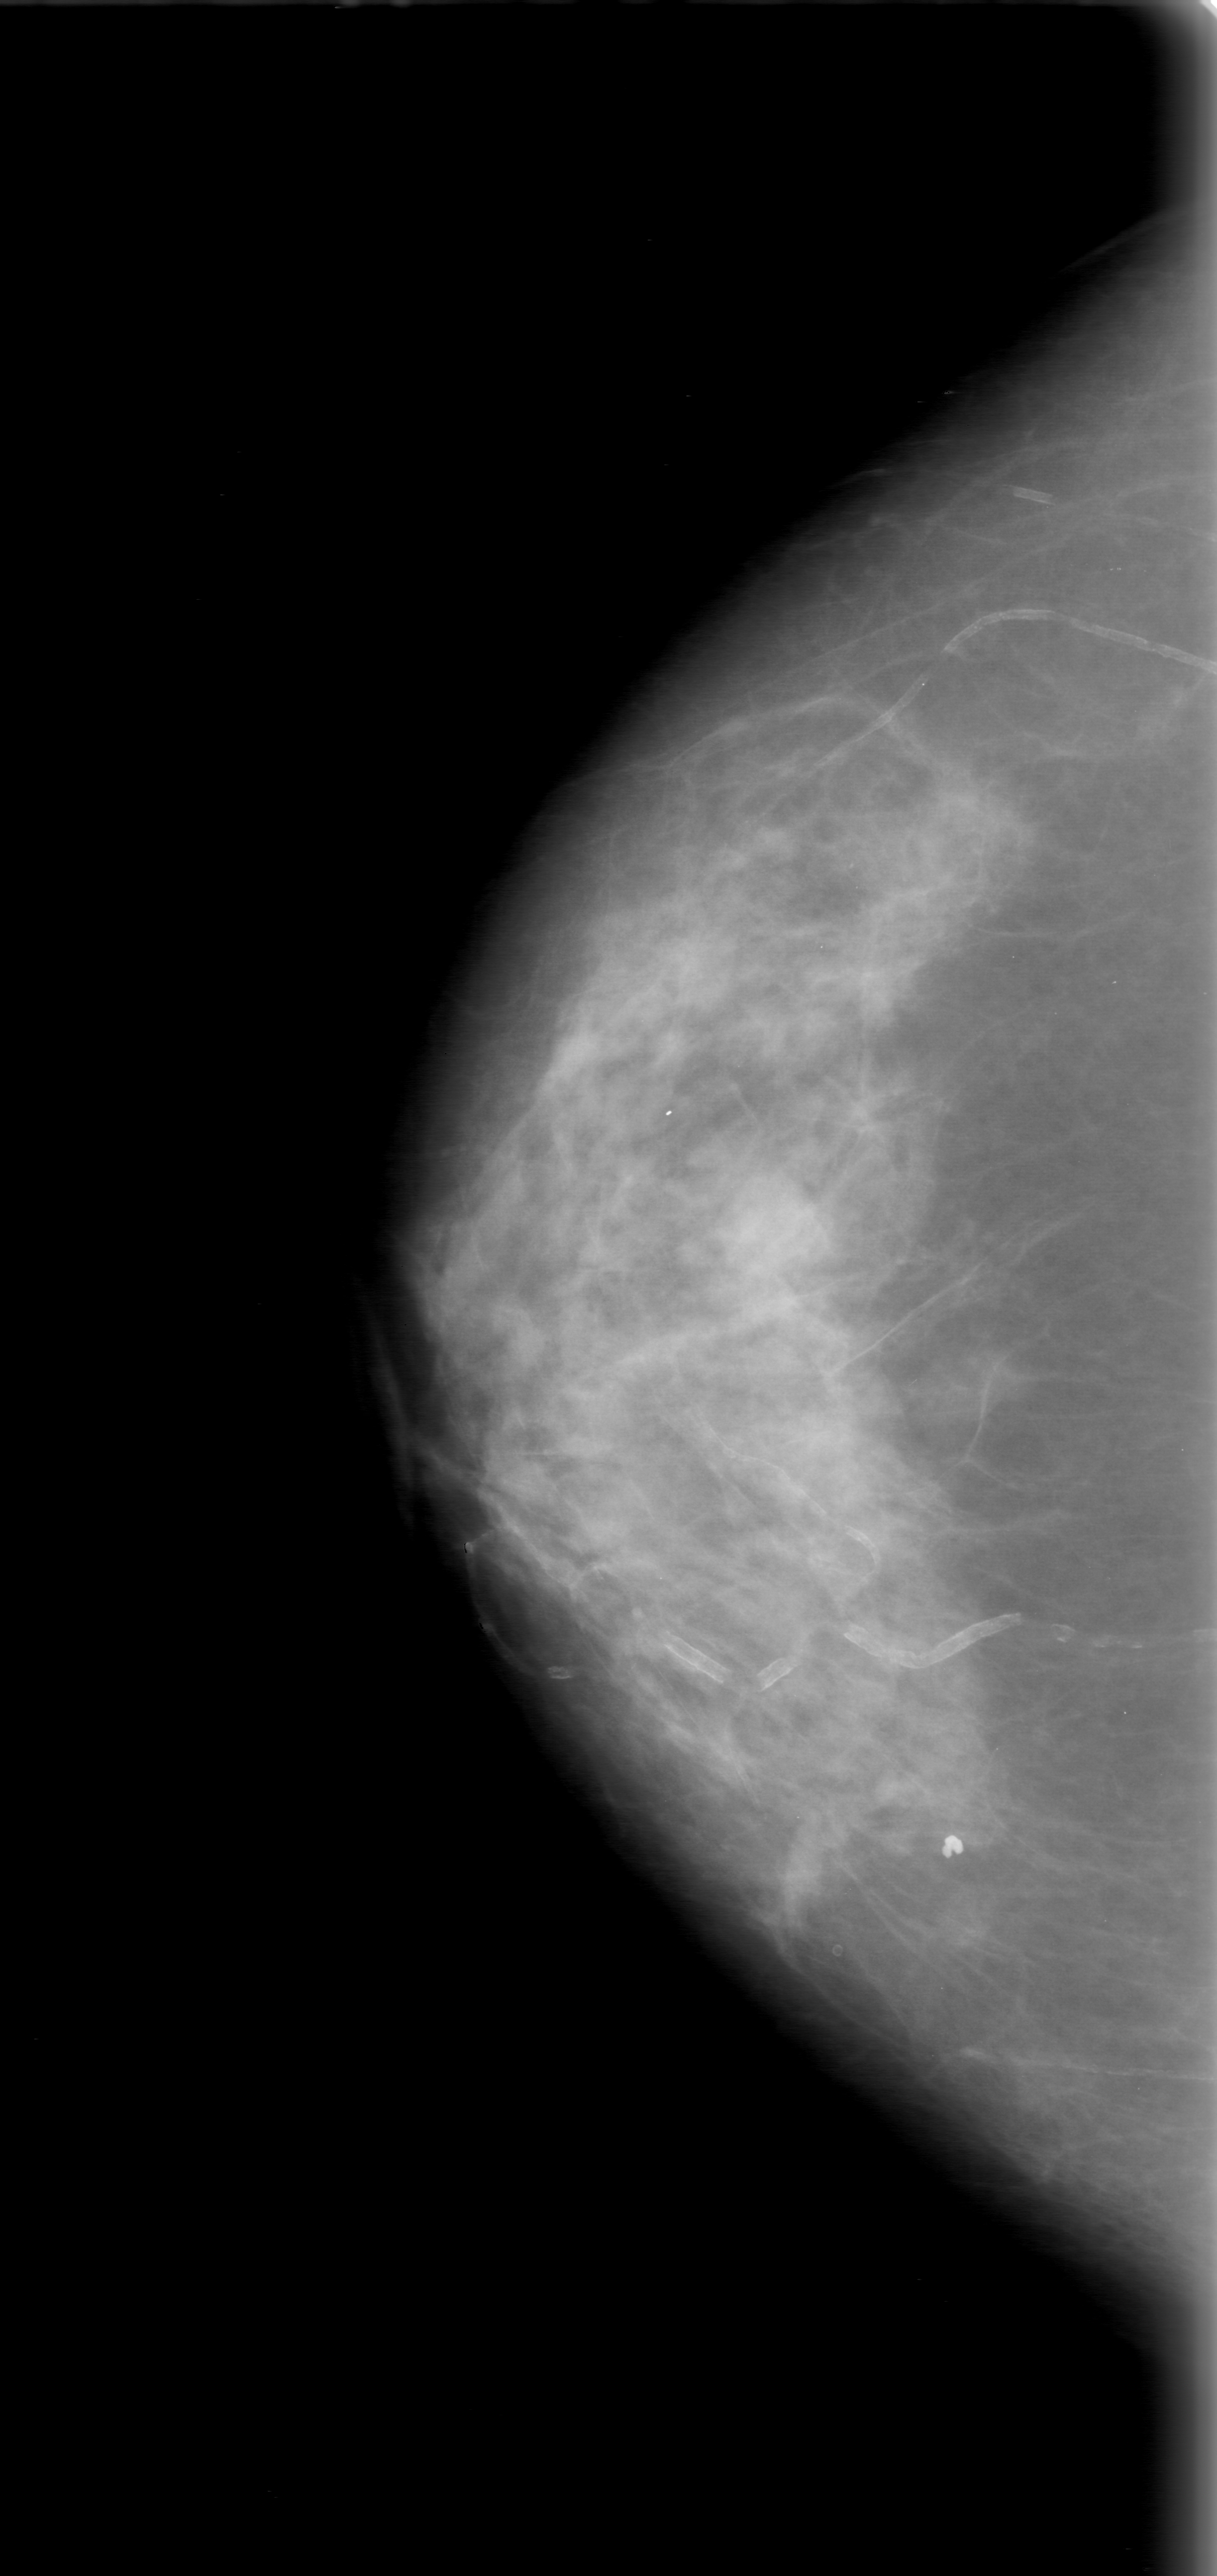
Scanned film-screen mammogram; right breast; craniocaudal (CC) view; BI-RADS breast density category 2 (scale 1–4).
Marked abnormality: mass, shape round, margins obscured; BI-RADS assessment category 0 (incomplete: needs additional imaging); subtlety rating 4 on a 1 (subtle) to 5 (obvious) scale; pathology result (as recorded, not read from the image): benign.